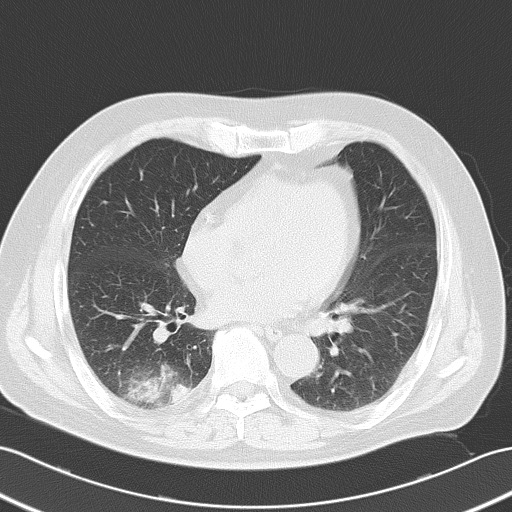
Chest CT, one axial slice. Slice 17 of 52 in the series (ordered by position). Reconstruction kernel B70f. 120 kVp. Lung window (W 1500 / L -600 HU). 5 mm slice thickness. 512 × 512 image matrix. Male patient, age 70 years. From the clinical record (not read from this slice): clinical TNM (as recorded): T2 N0 M0; histopathological grade: G2.
Structures marked on this image (rectangle marked by the reading radiologist):
- lung tumour (recorded histology: adenocarcinoma): bounding box [x1, y1, x2, y2] px = [122, 360, 187, 409]